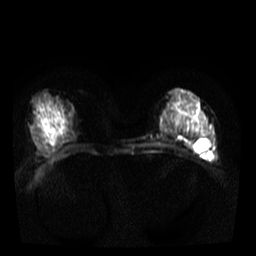
Breast MRI, one axial slice; position 18 of 40 along the scan axis; diffusion-weighted series; image 2 of 4 stored at this slice position (different b-values; order by instance number); 3 T; 5 mm slice thickness; 256 × 256 image matrix, field of view 320 × 320 mm. Female patient.
Annotated regions visible in this slice (outlined manually by an expert reader):
- tumour on diffusion-weighted imaging: bounding box <213,154,216,161> (left, top, right, bottom; pixels)